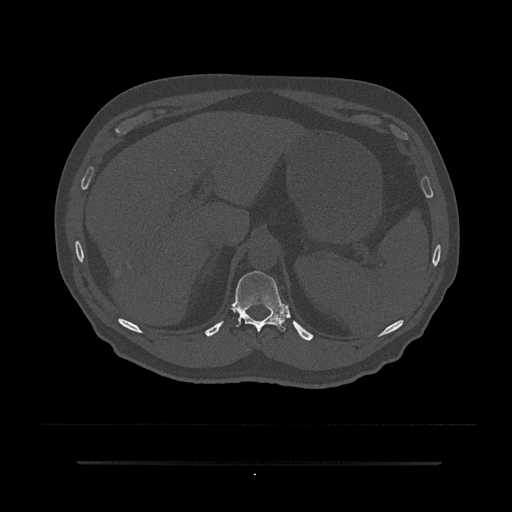
CT including the spine, one axial slice; slice 269 of 797 in the series (ordered by position); reconstruction kernel Br40s/3; bone window (W 1800 / L 400 HU); 0.5 mm slice thickness; 512 × 512 image matrix, field of view 464 × 464 mm. Male patient, age 59 years. Case-level facts recorded for this patient, not image findings: primary cancer: bile ducts; vertebrae with lytic lesions (as recorded): T10.
Outlined on this slice (semi-automatic segmentation, software-assisted and operator-edited):
- T11 vertebra: box from (x=233, y=271) to (x=286, y=332) px